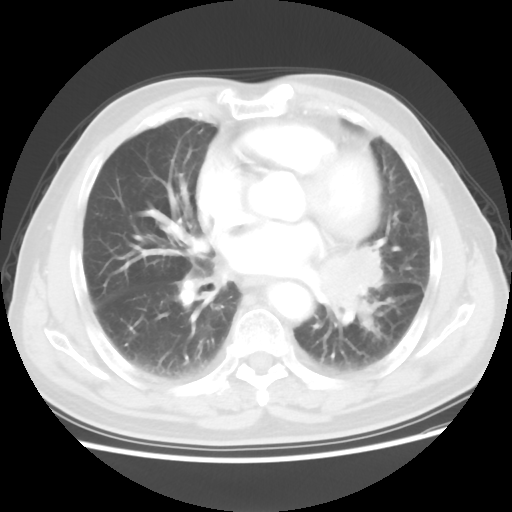
Chest CT, one axial slice. Slice 28 of 56 in the series (ordered by position). Reconstruction kernel STANDARD. 120 kVp. Lung window (W 1500 / L -600 HU). 5 mm slice thickness. 512 × 512 image matrix, field of view 360 × 360 mm. Male patient, age 75 years. Case-level facts recorded for this patient, not image findings: clinical TNM (as recorded): T3 N0 M0.
Outlined on this slice (bounding box drawn by a radiologist):
- lung tumour (recorded histology: squamous cell carcinoma): bounding box [x1, y1, x2, y2] px = [308, 239, 390, 318]